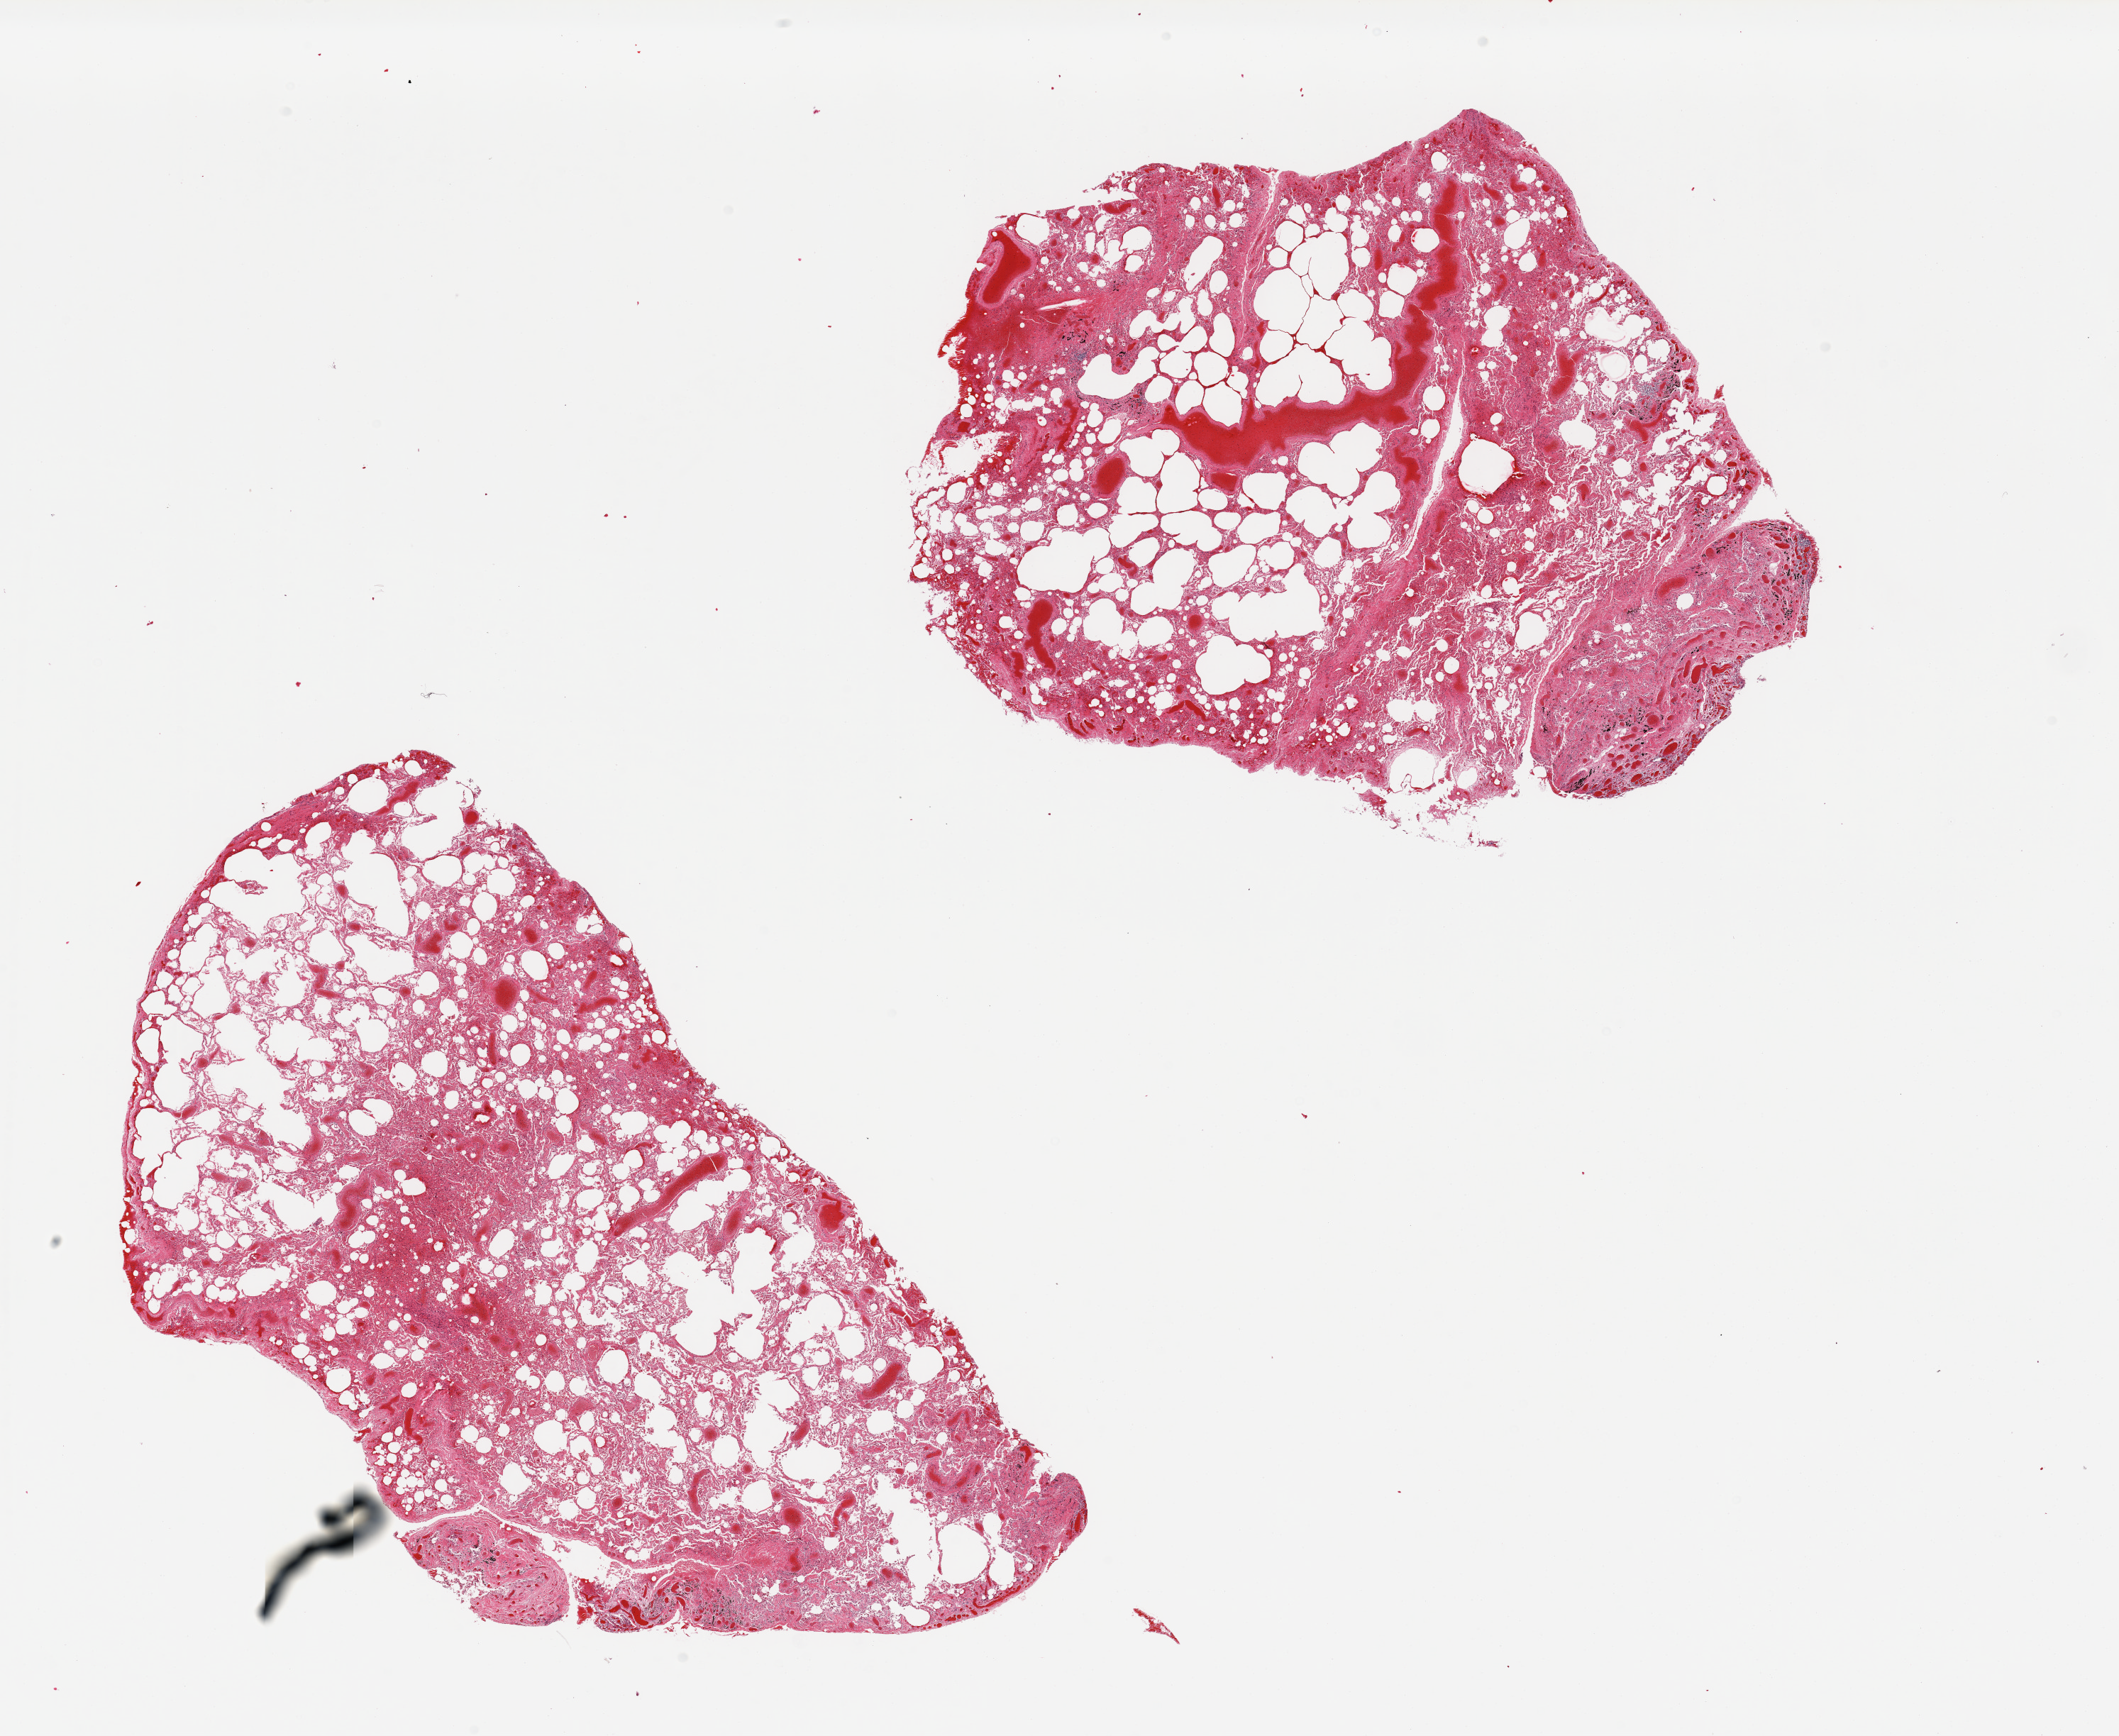
Digitized hematoxylin and eosin (H&E)-stained section, a low-resolution overview of the entire scanned area, about 23.6 x 19.4 mm. PAXgene-fixed paraffin-embedded (PFPE) section. Target tissue: lung. Donor tissue sample.
Pathologist's review note for this sample: 2 pieces; emphysema, hemorrhage, fibrosis, carbon deposits.